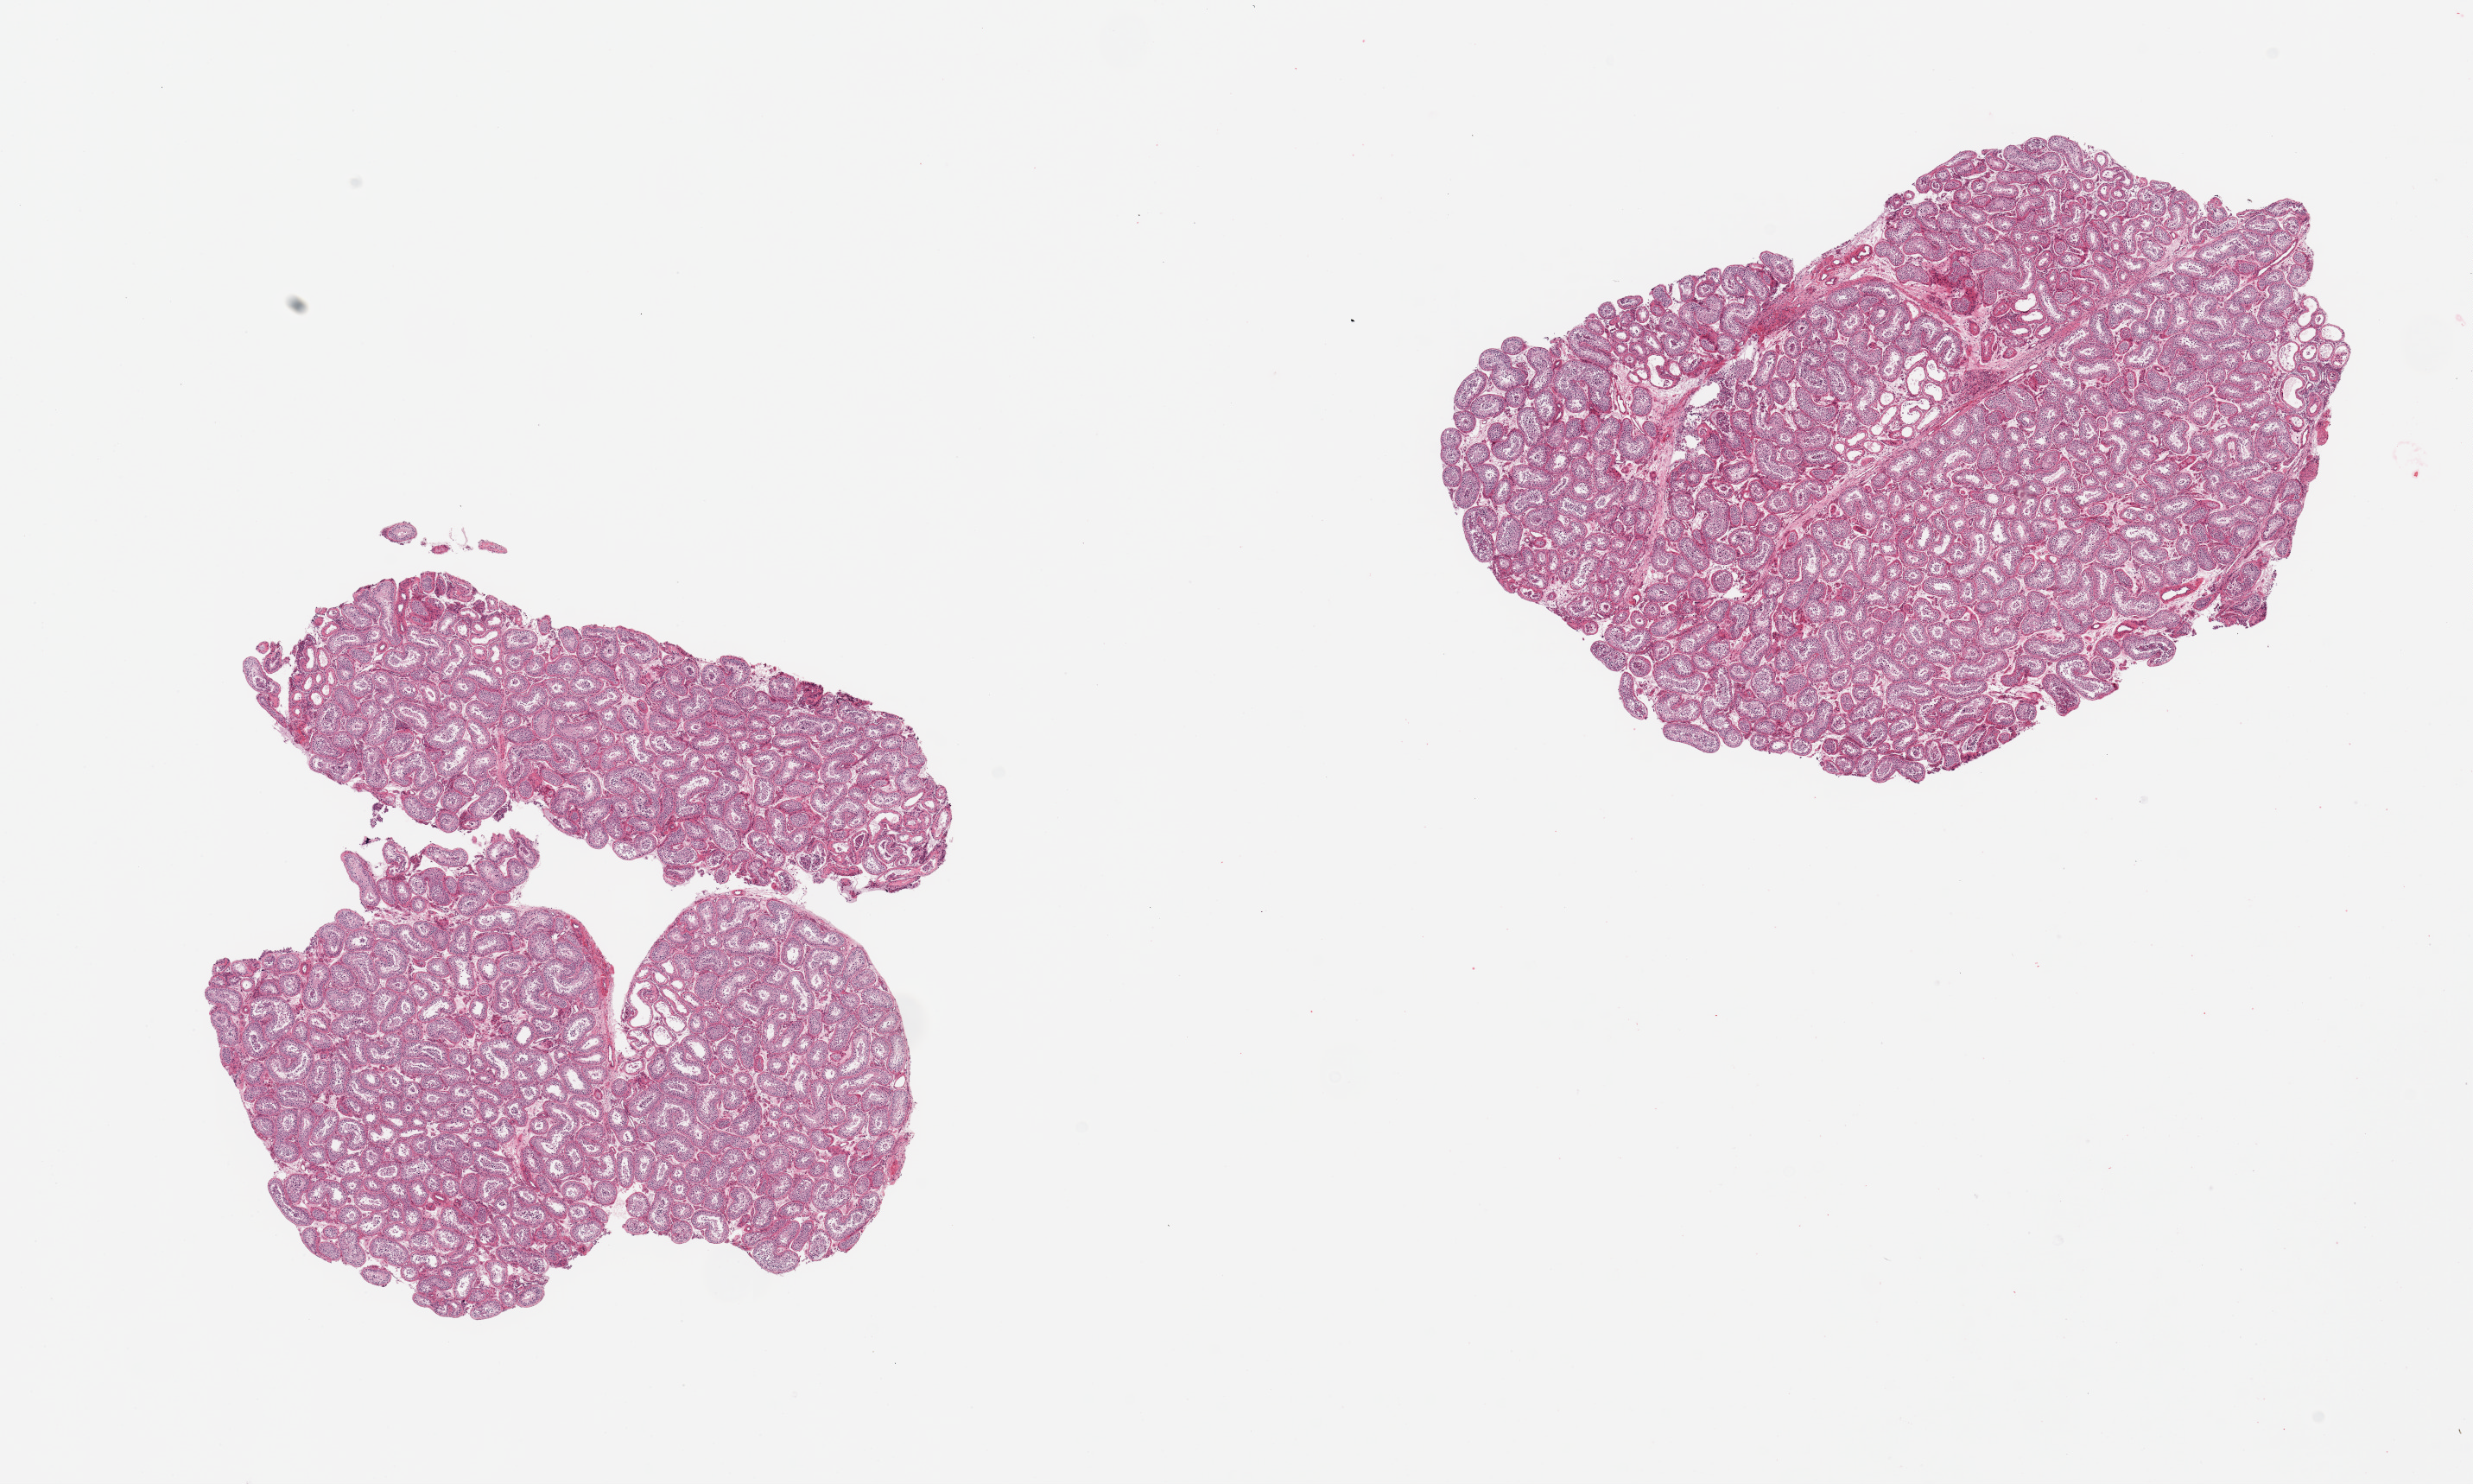
Haematoxylin and eosin whole-slide image, shown as a low-resolution overview of the whole scanned area (about 22.6 x 13.6 mm). PAXgene-fixed, paraffin-embedded tissue. Sampled site (target tissue): testis. Tissue donor sample.
Reviewer comment on this tissue sample: 2 pieces; active spermatogenesis.